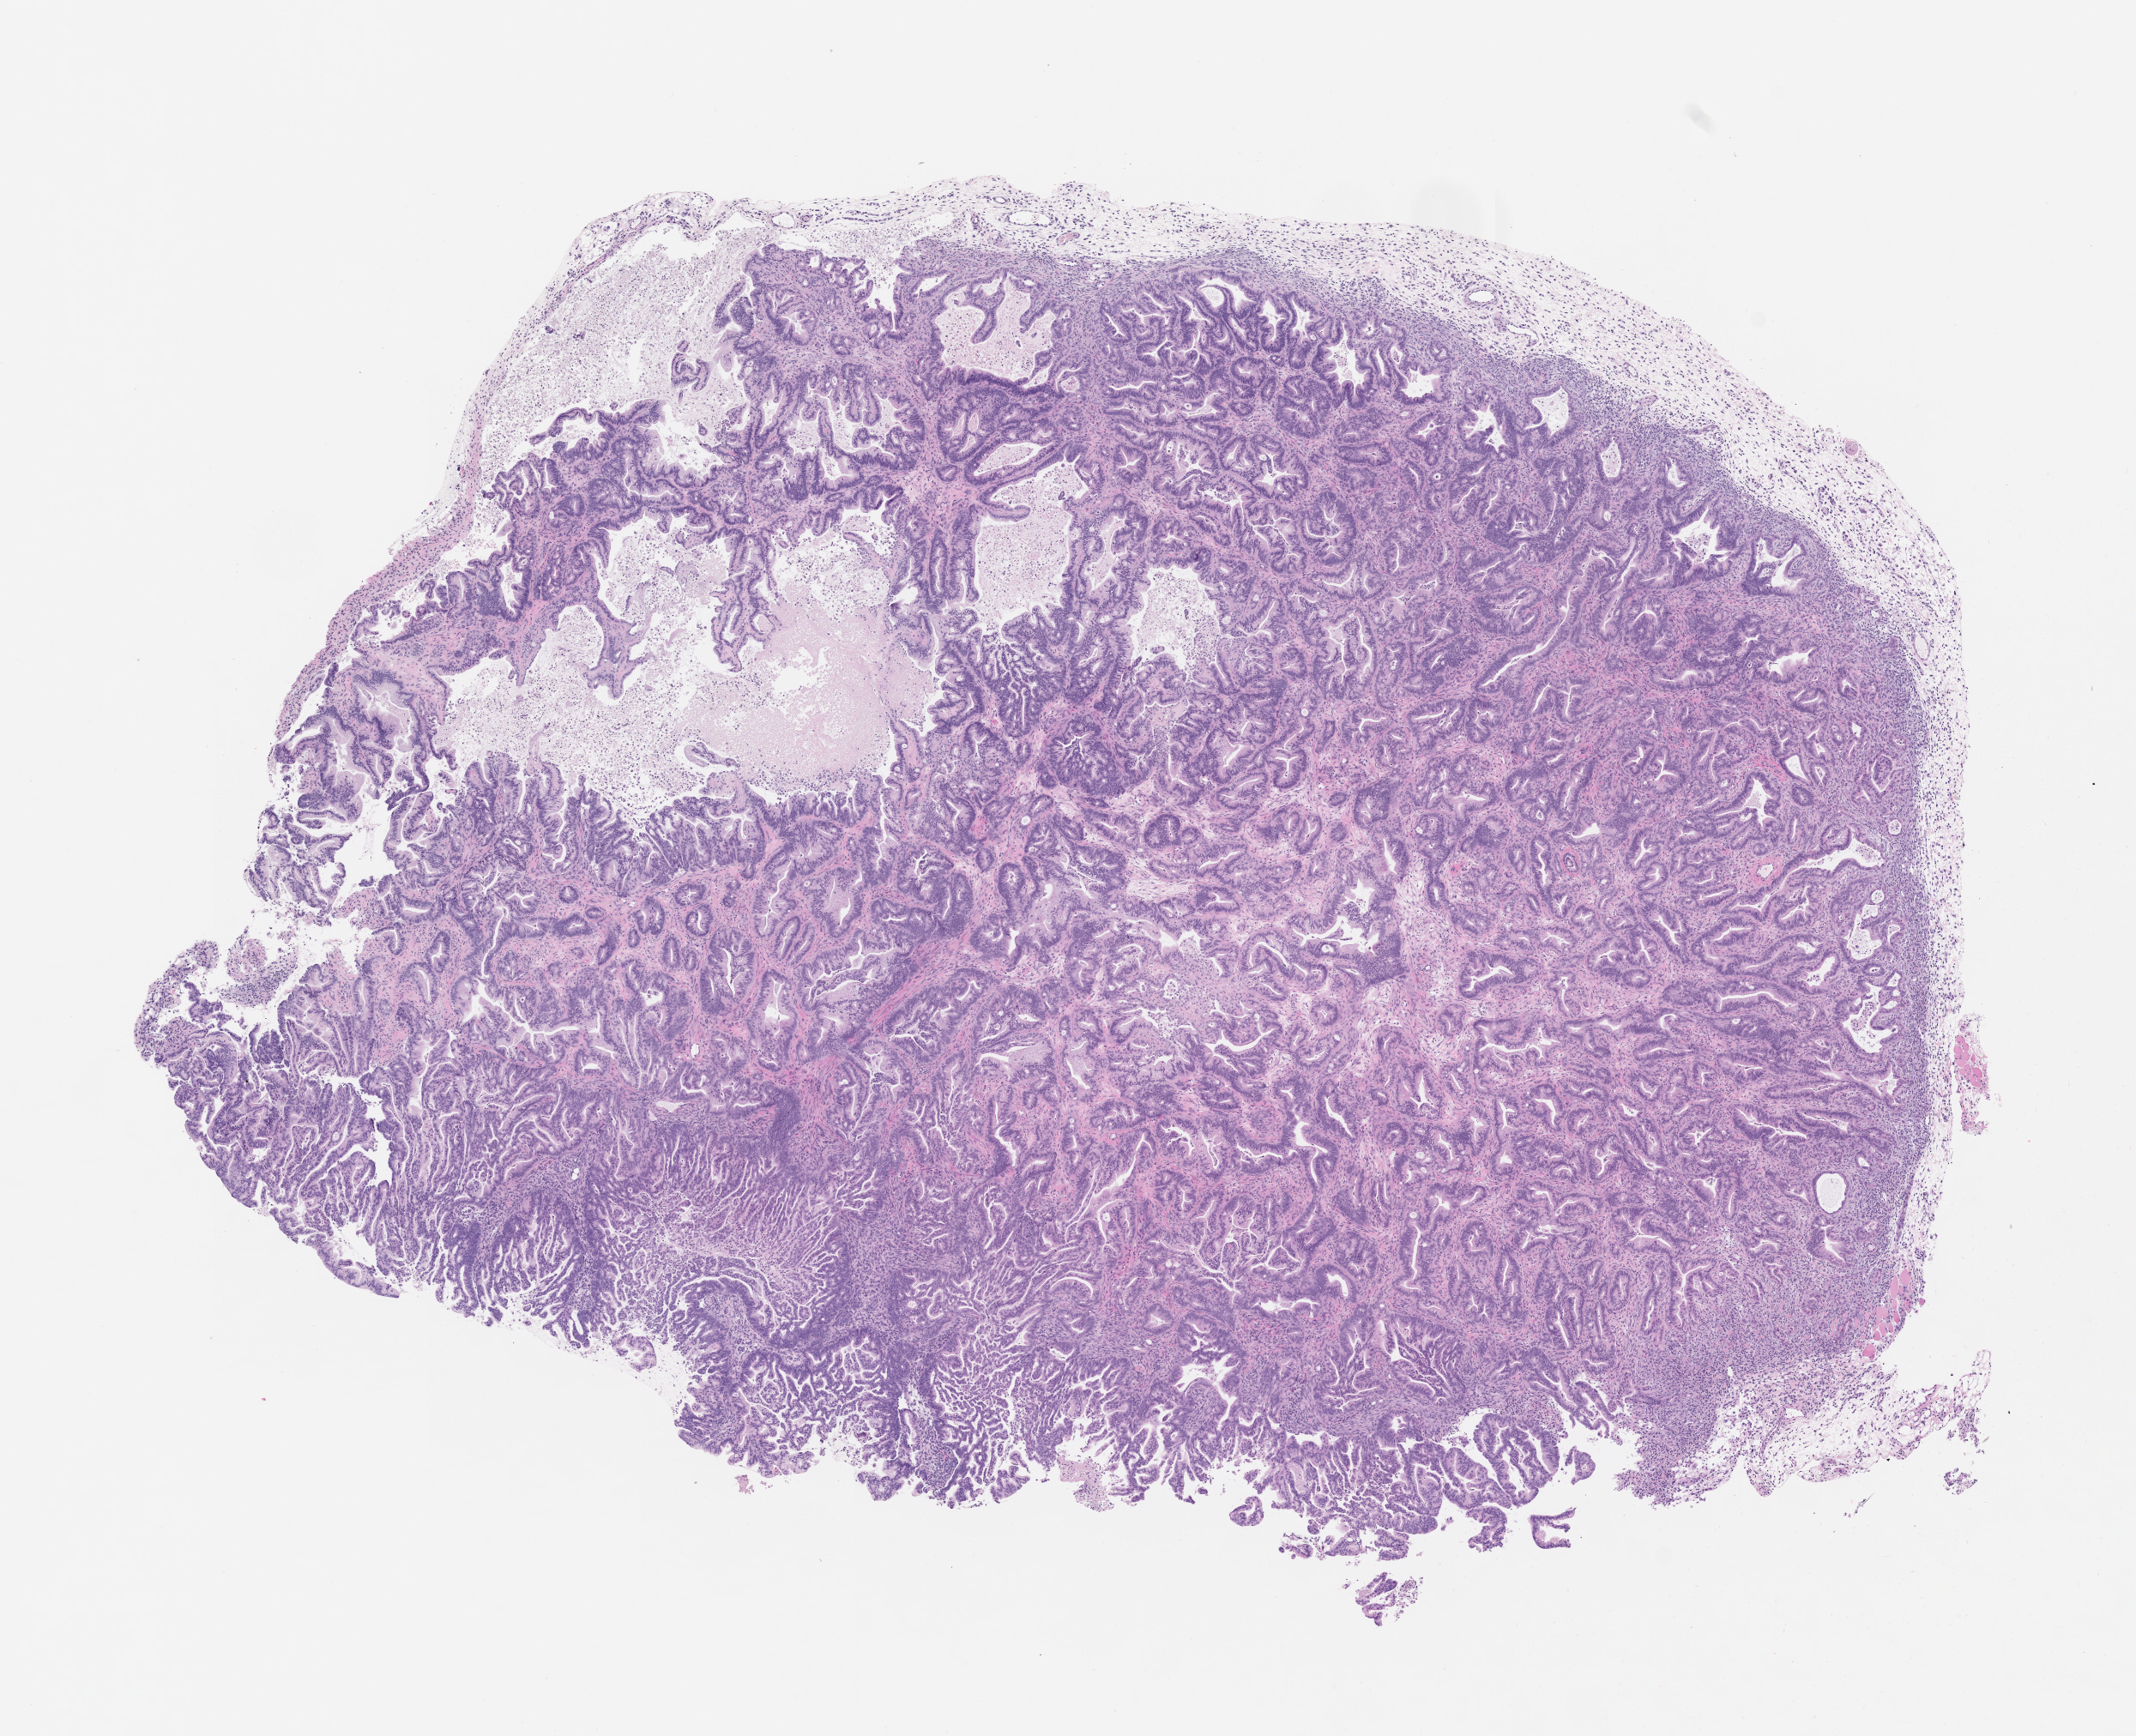
Whole-slide image, H&E: patient-derived xenograft (human tumor grown in a mouse), passage 1, whole scanned area (about 10.0 x 8.1 mm) shown as a low-resolution overview; formalin-fixed paraffin-embedded section; originating tumor site category: pancreas.
Originating patient diagnosis: Pancreatic Adenocarcinoma.